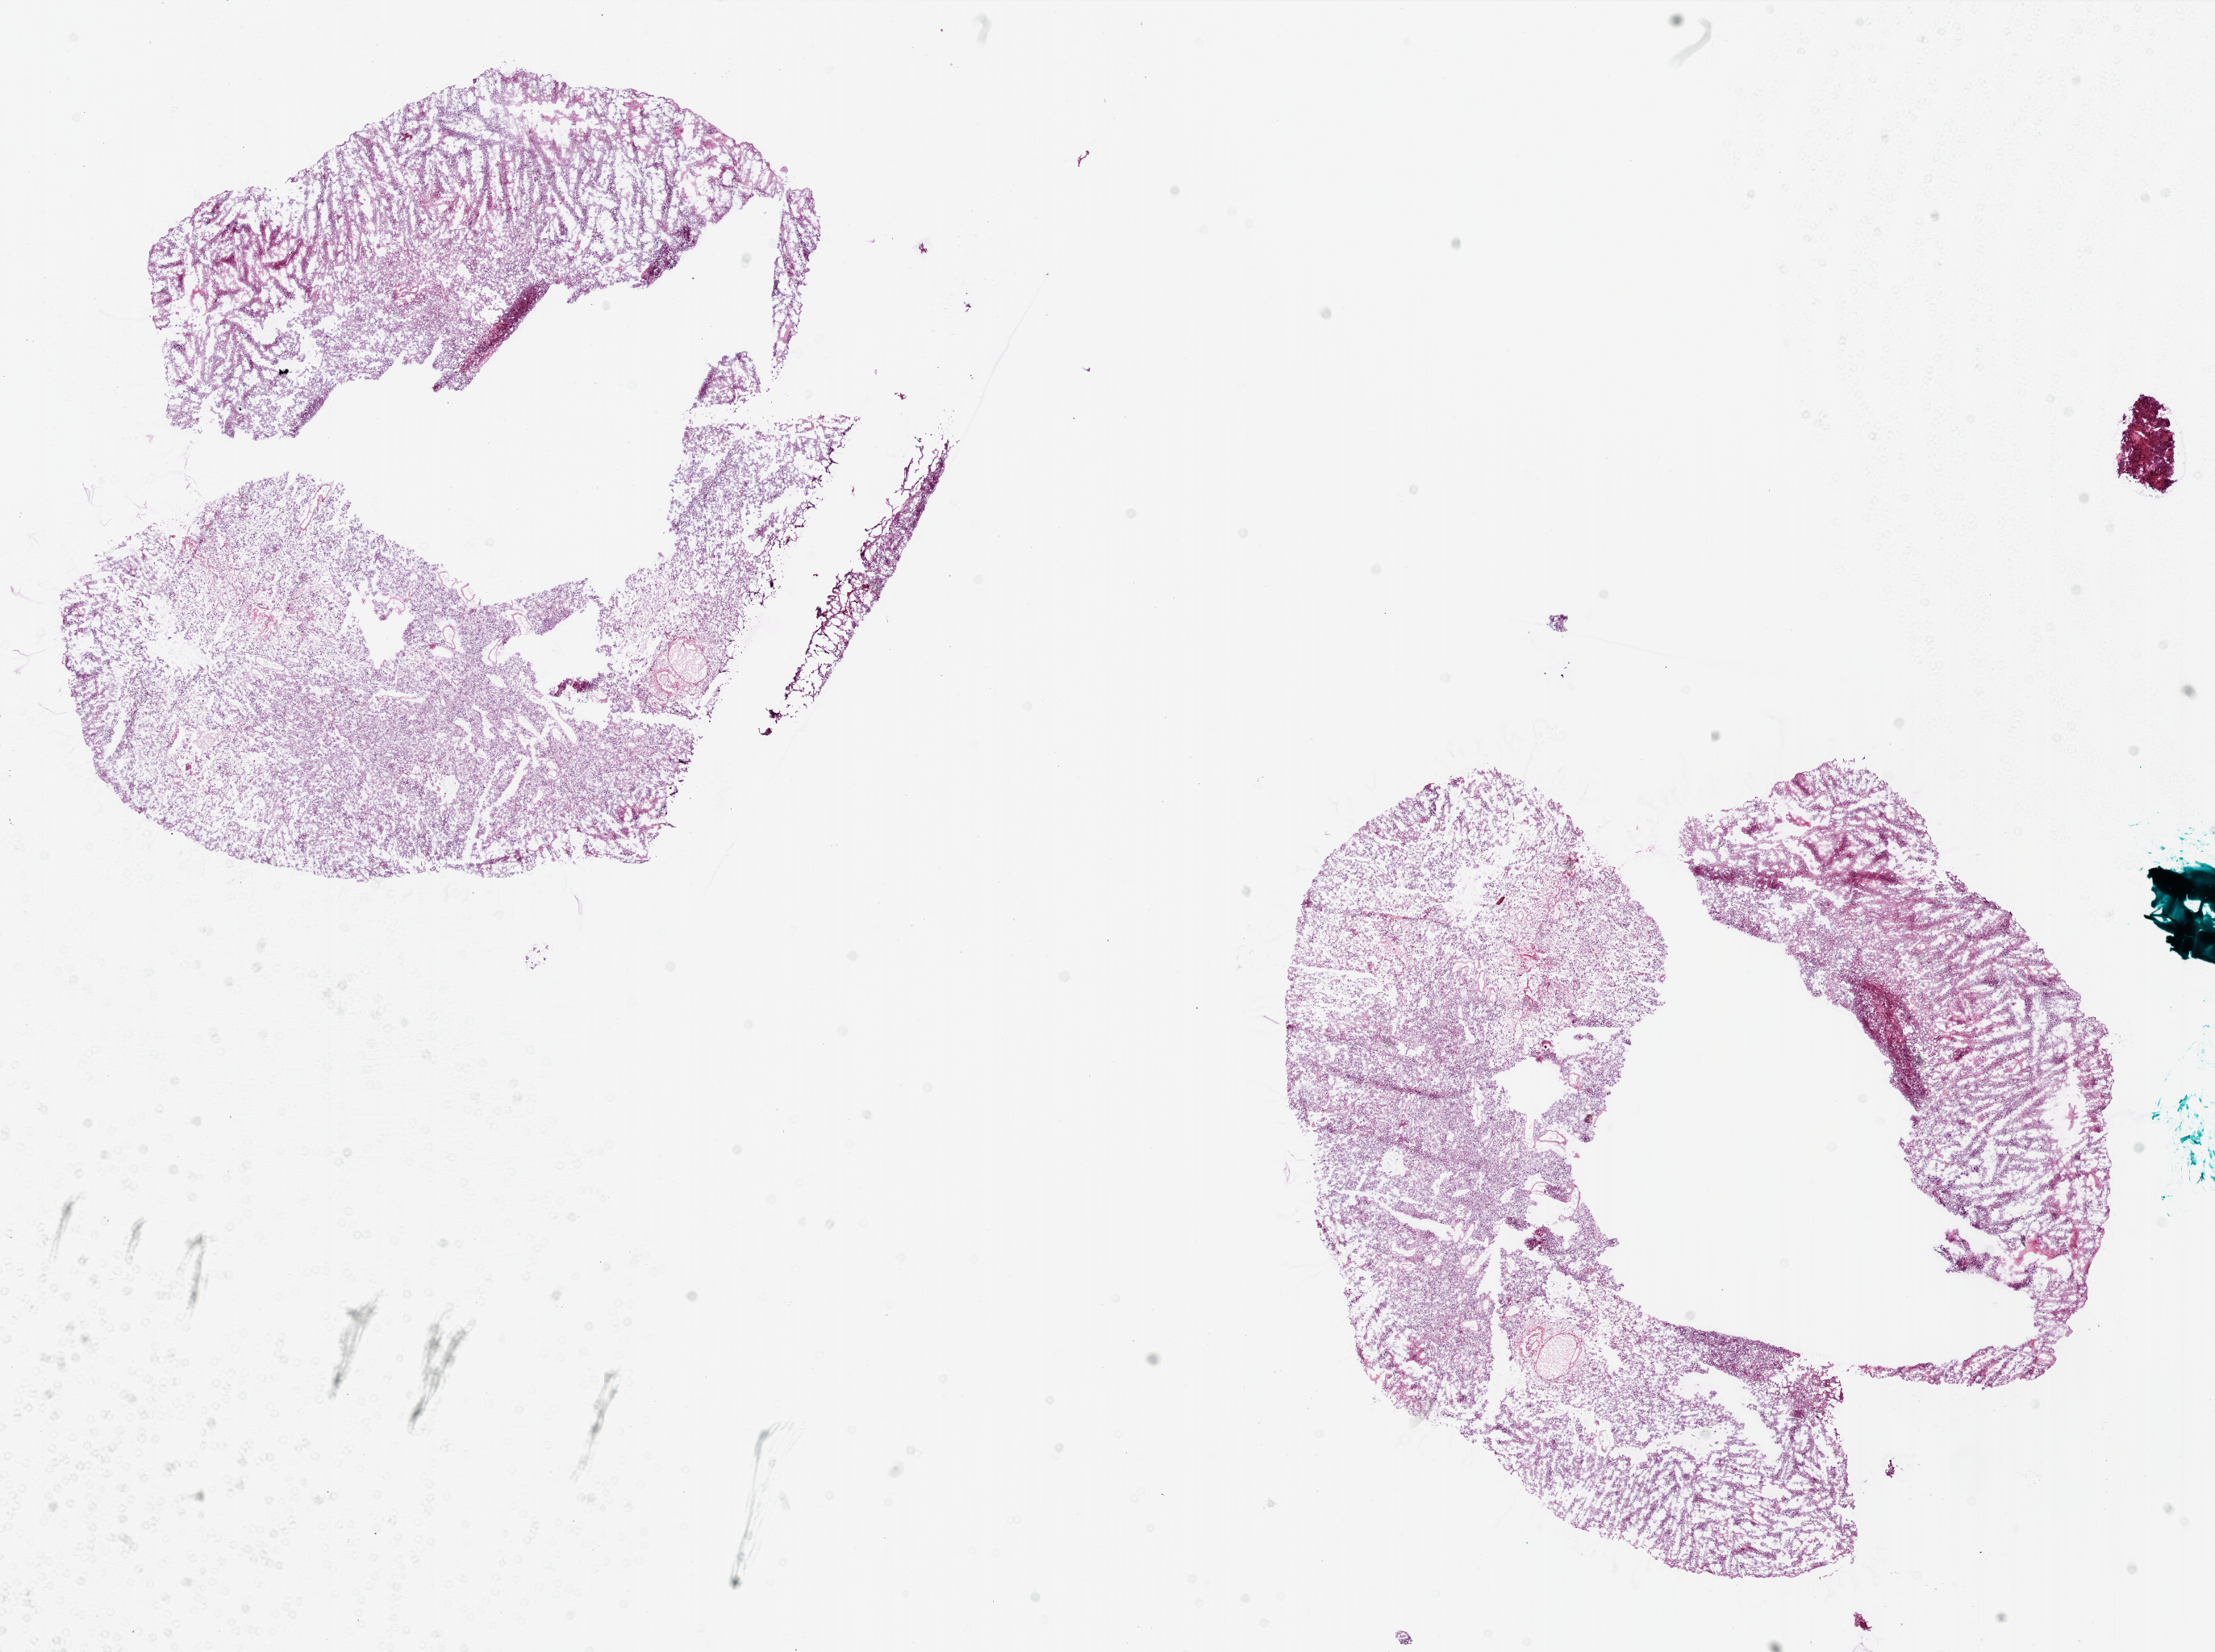
H&E whole-slide image — whole scanned area (about 22.0 x 16.4 mm) shown as a low-resolution overview. Frozen section from the bottom of the tissue portion. Brain, primary tumour sample. Patient: female, age at initial diagnosis 45 years. Pathologist review of this section (percent, as recorded): tumour cells 95%, tumour nuclei 100%, normal cells 0%, stromal cells 0%, necrosis 5%. Inflammatory infiltration, as recorded: lymphocyte infiltration 0%.
Diagnosis: Glioblastoma.